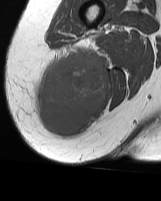
MRI of an extremity soft-tissue mass, one axial slice. Position 20 of 70 along the scan axis. MR volume resampled by the dataset authors to the PET/CT grid (not the native acquisition matrix). 3.27 mm slice thickness. 161 × 201 image matrix. Female patient. Case-level facts recorded for this patient, not image findings: histological type: synovial sarcoma; grade: intermediate; site of the primary tumour: right buttock.
Outlined on this slice (expert contour drawn on MRI and transferred to this co-registered scan by the dataset authors):
- gross tumour volume including surrounding oedema: box from (x=35, y=45) to (x=107, y=137) px
- gross tumour volume (mass): (x=35, y=52)–(x=107, y=137)